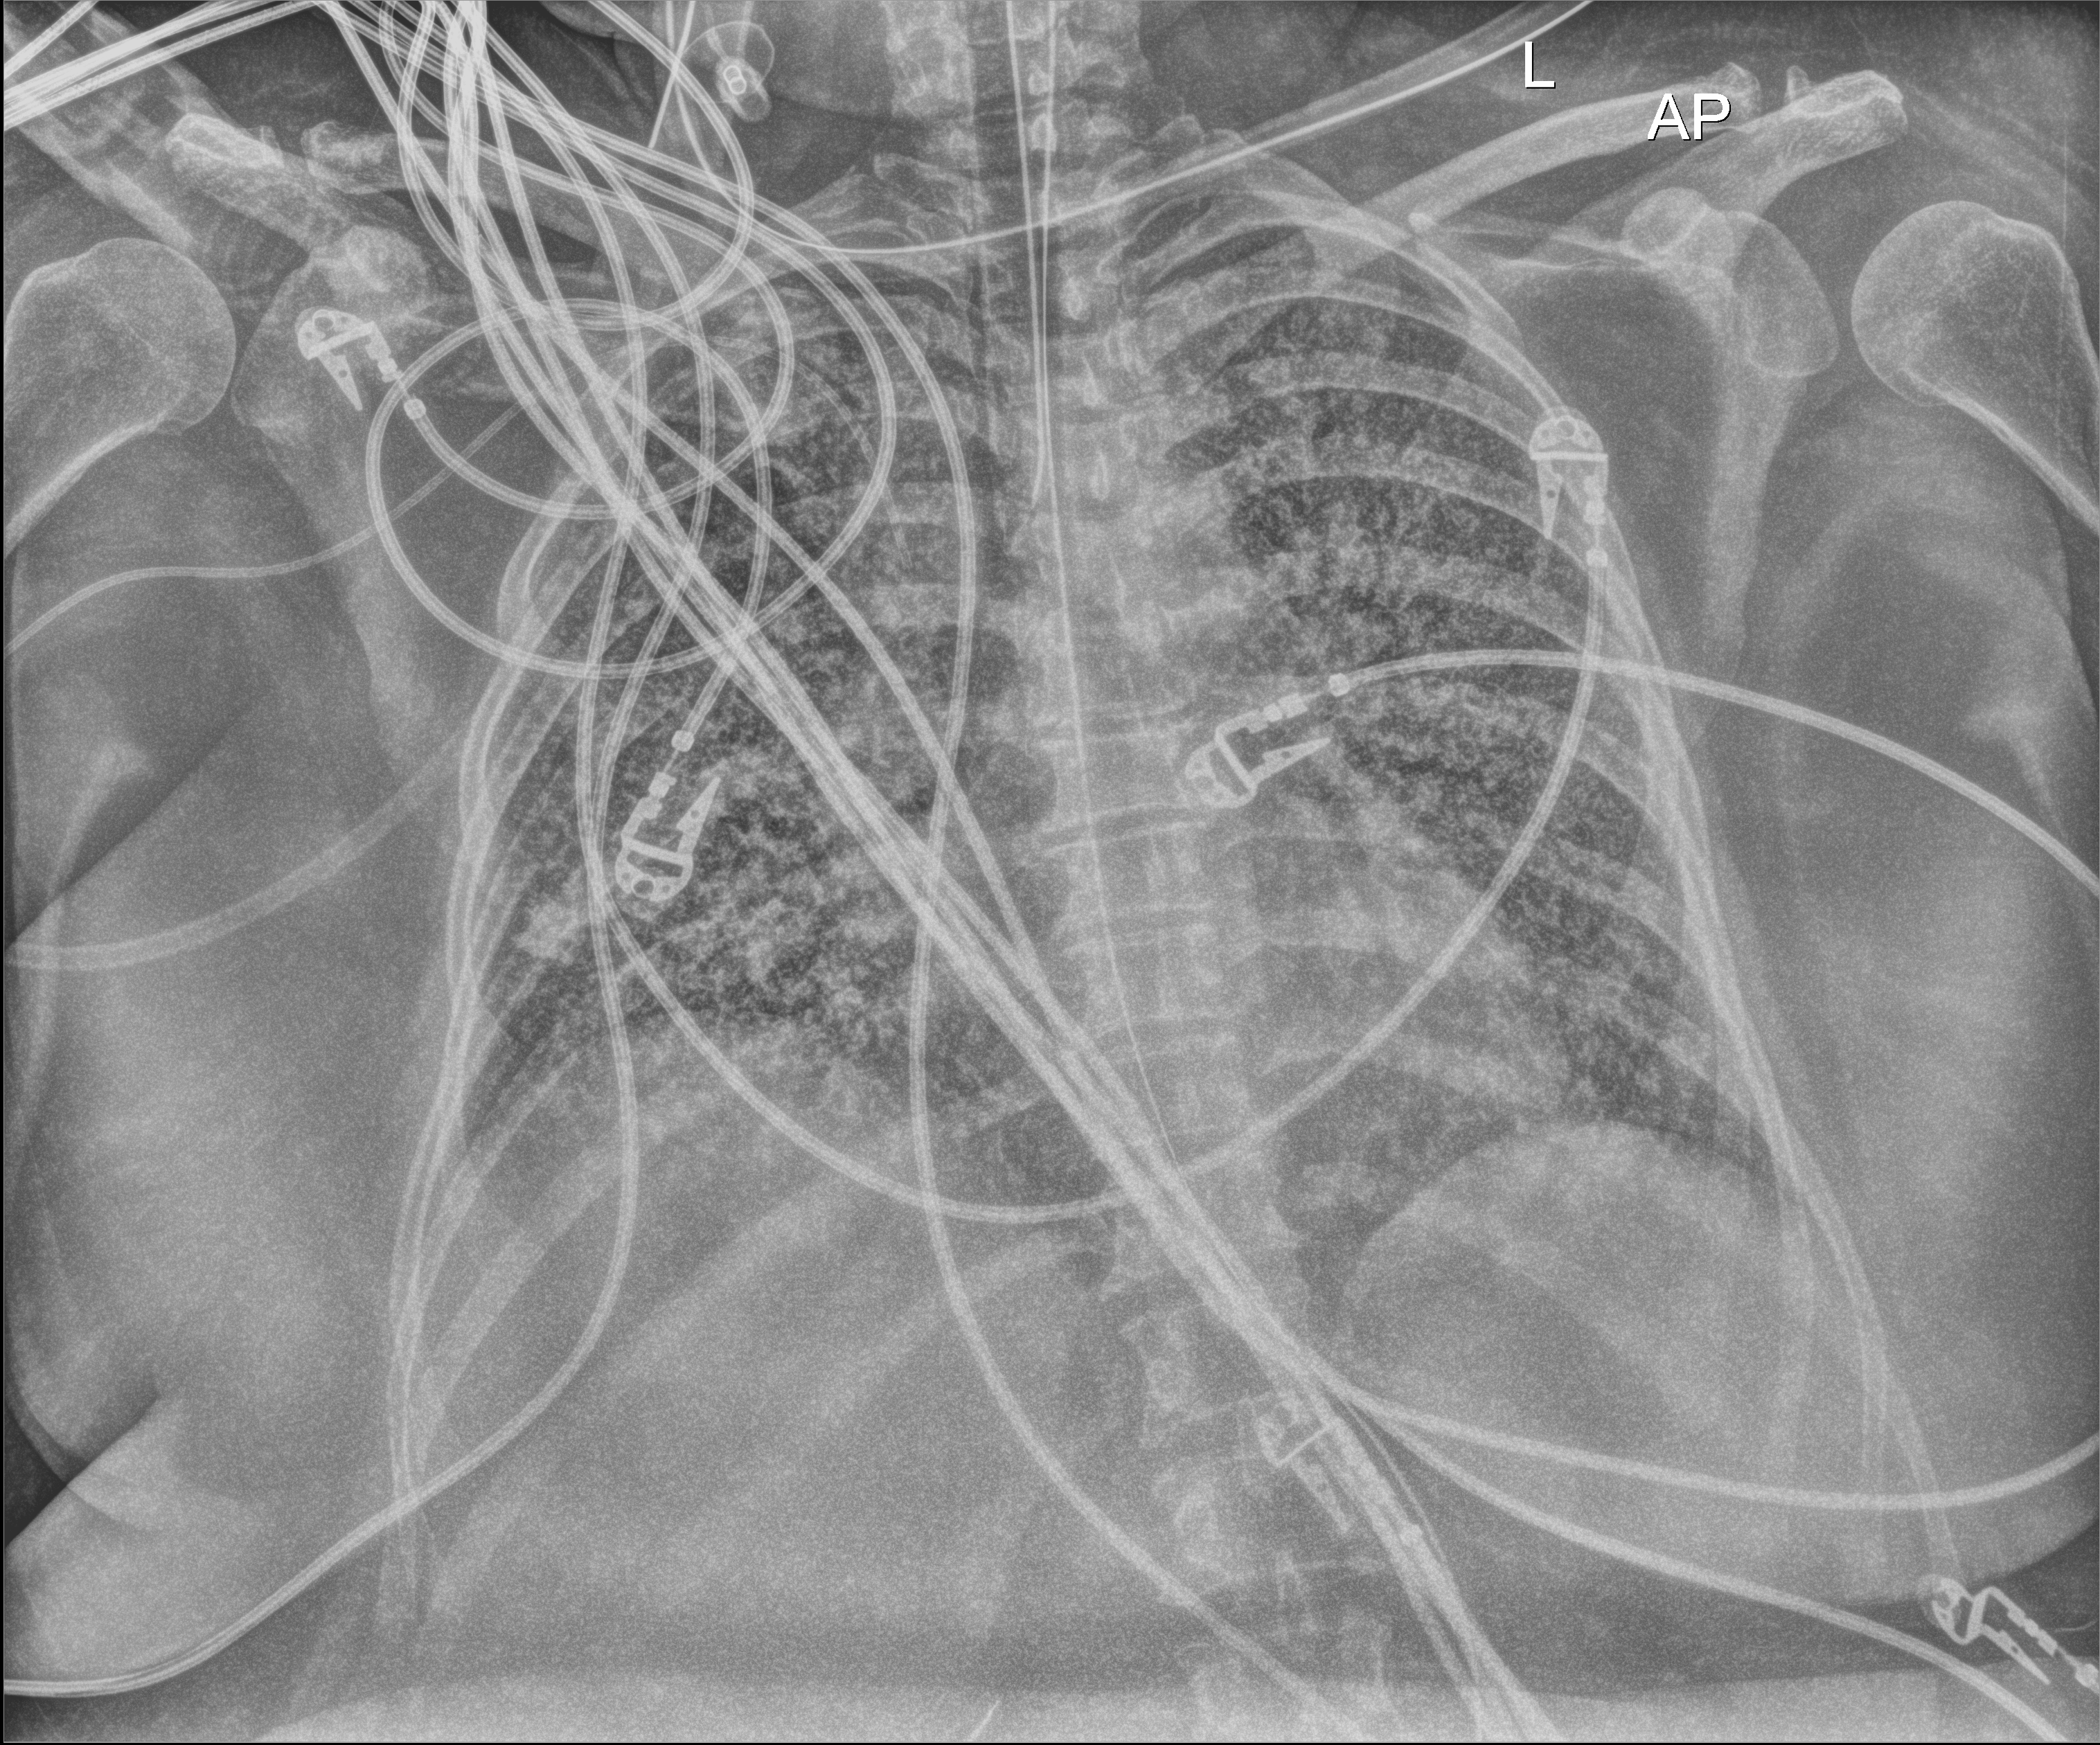
Bedside chest radiograph (digital radiography), anteroposterior (AP) projection. Female patient hospitalised with COVID-19, age 18–59 years.
Hospital-stay facts (about this admission, not read from this image; timing relative to this image not recorded):
- chronic kidney disease (admission record): no
- diabetes (admission record): no
- admitted to intensive care during this hospital stay: yes